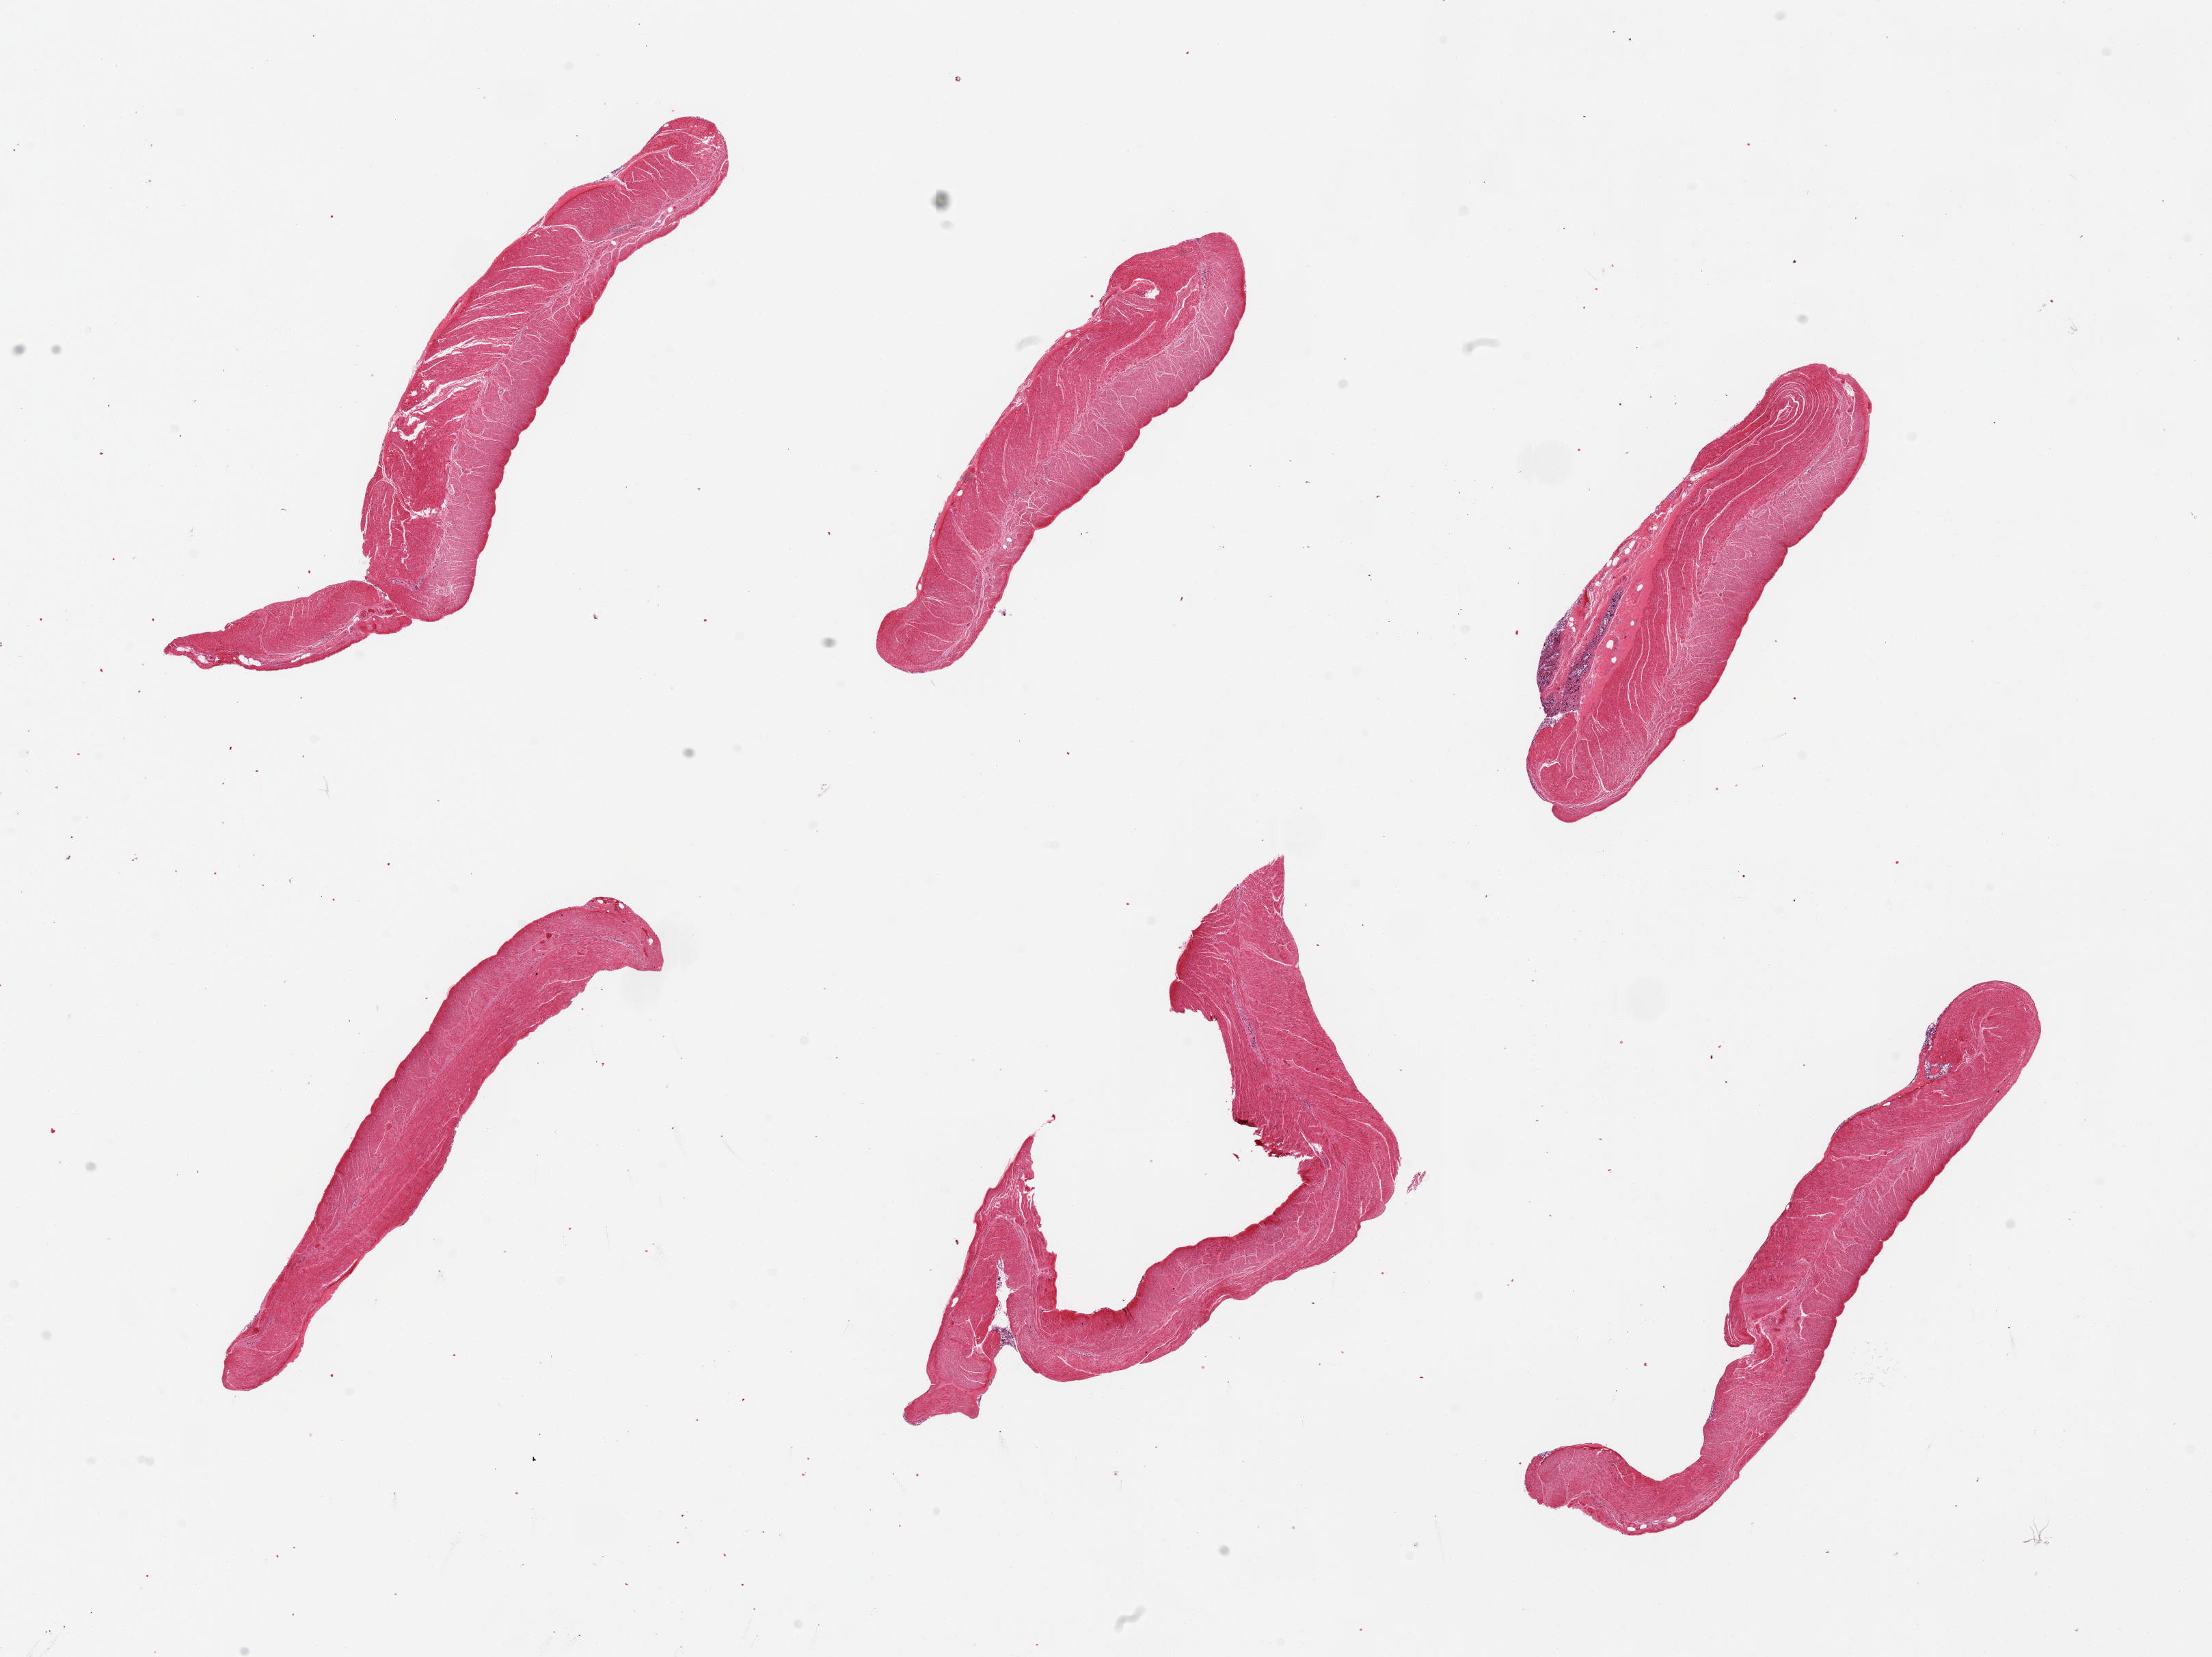
Hematoxylin and eosin (H&E) whole-slide image, brightfield — low-resolution overview of the scanned area, about 25.6 x 19.2 mm (acquisition: 20x scan). PAXgene-fixed paraffin-embedded (PFPE) section. Sampled site (target tissue): sigmoid colon. Tissue donor sample. Donor: female.
Reviewer comment on this tissue sample: 6 pieces, all muscularis.